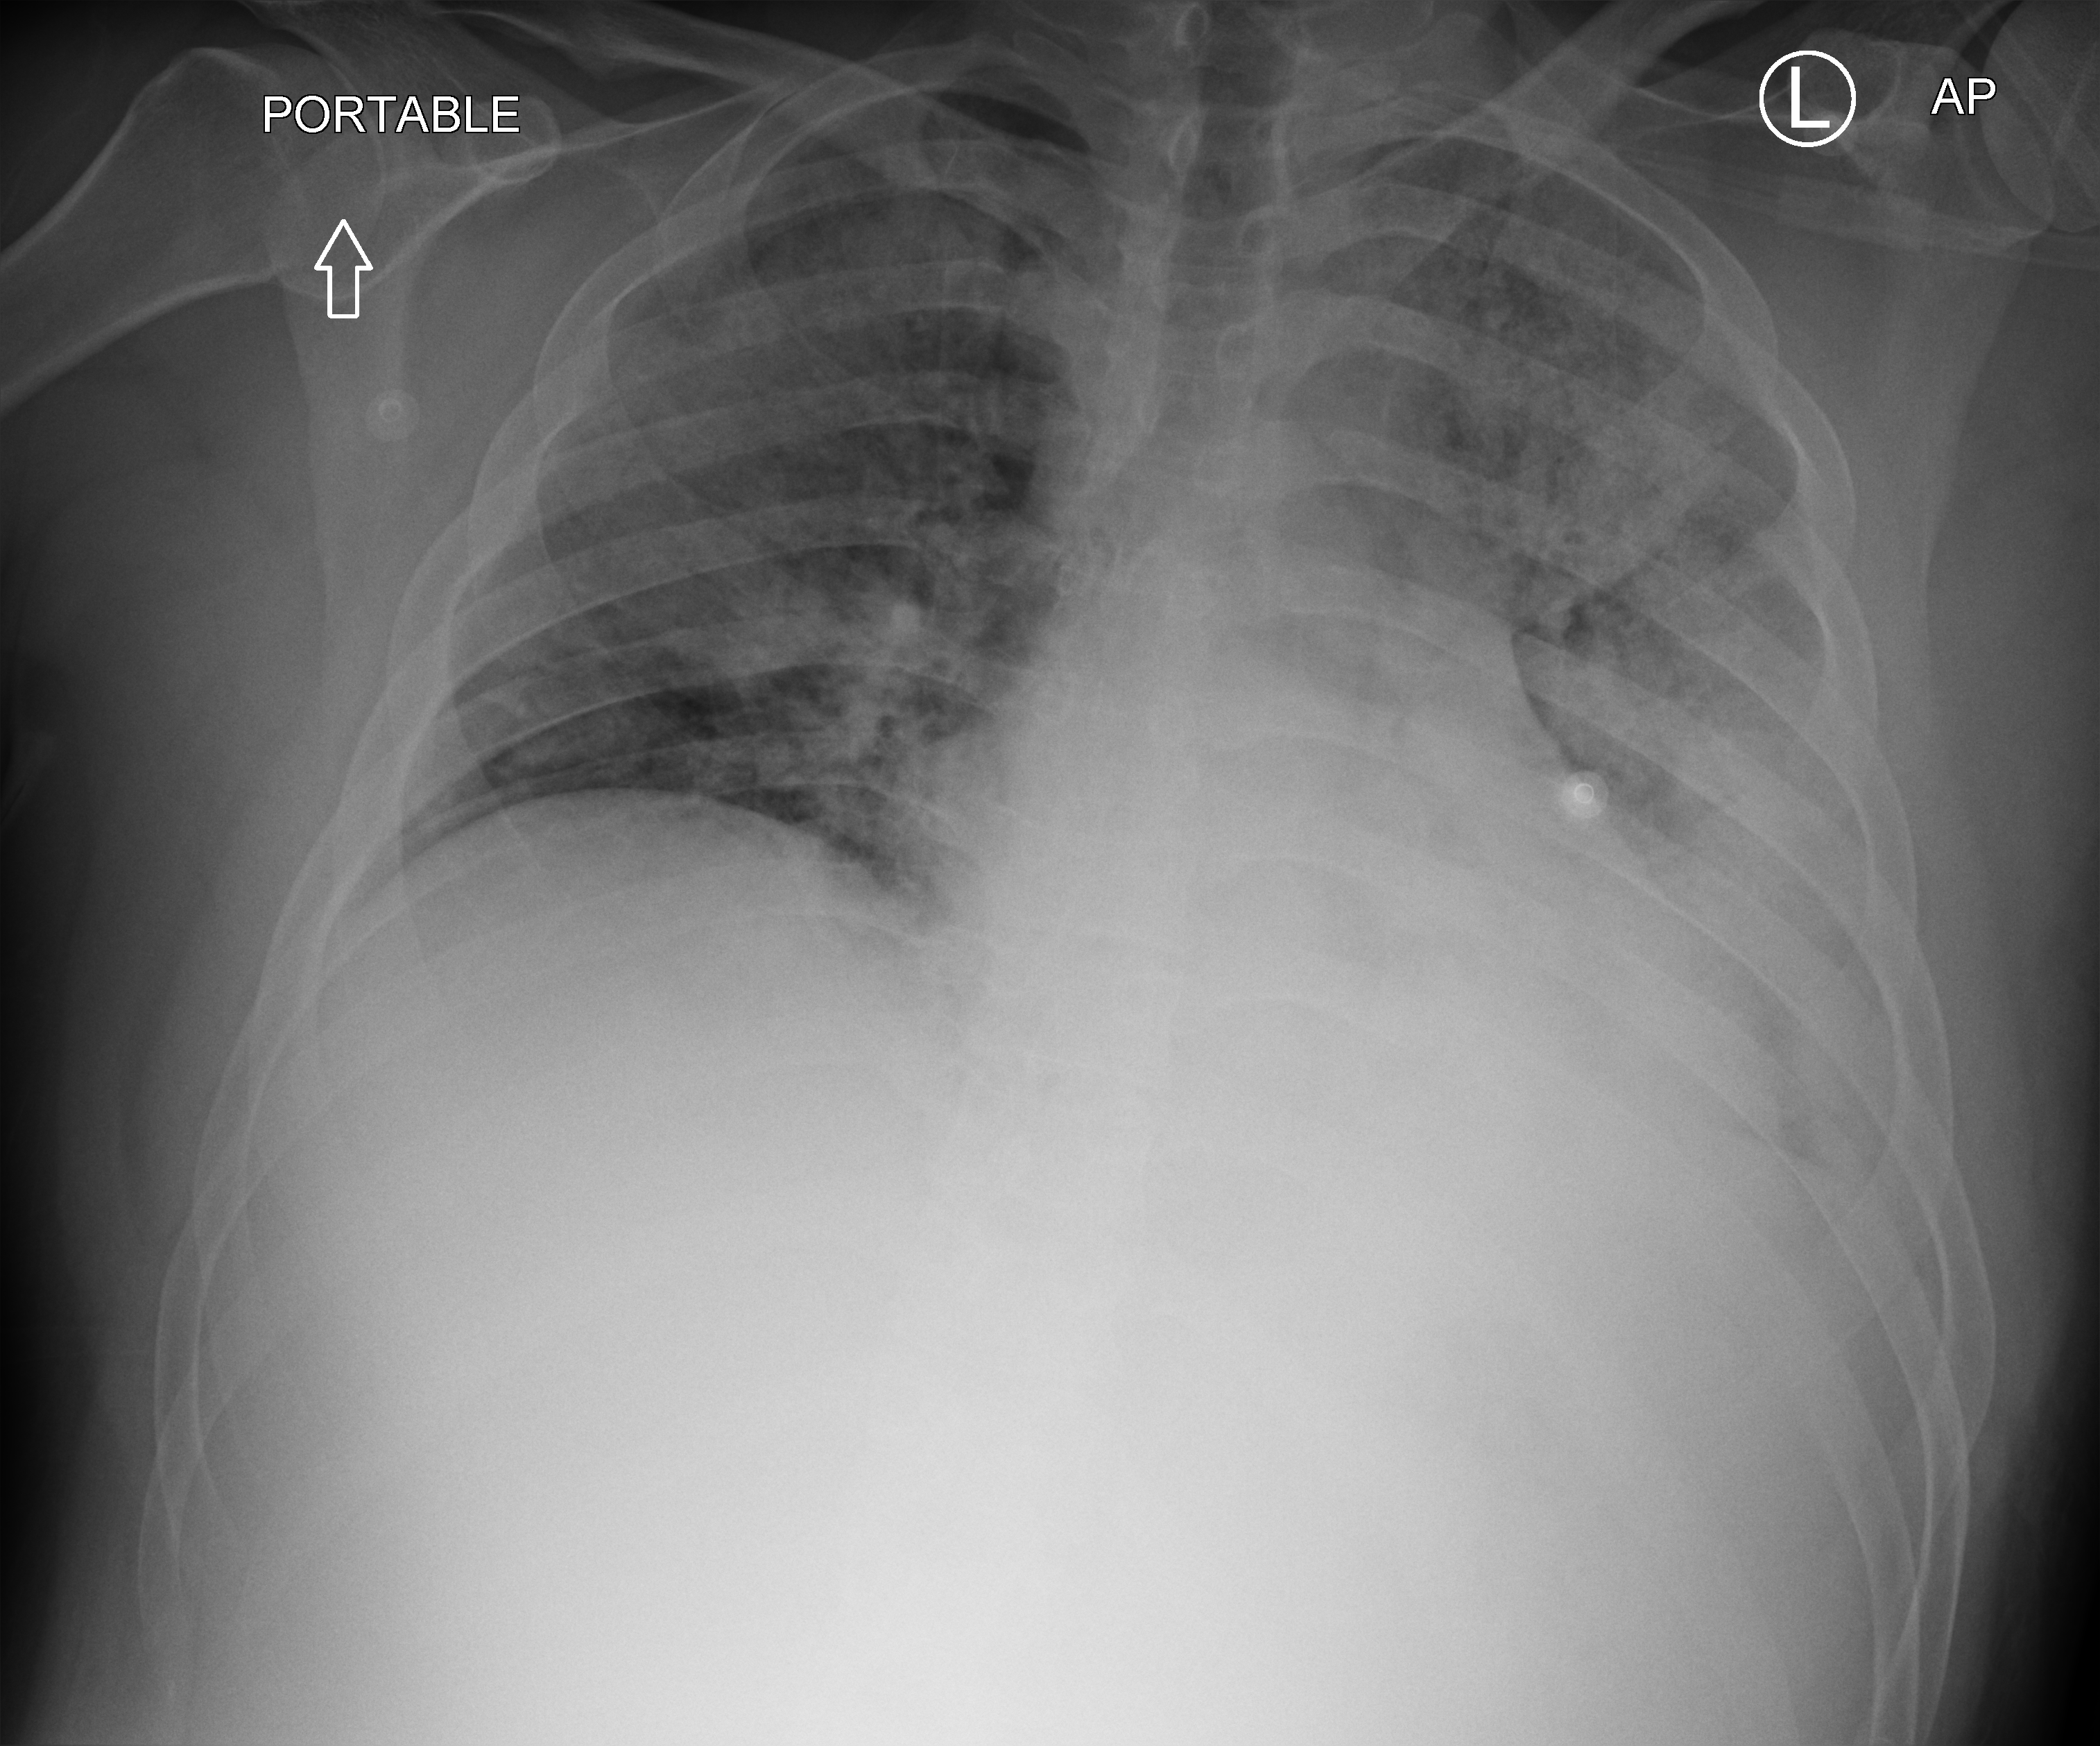
Portable chest radiograph, anteroposterior (AP) projection. Patient hospitalised with COVID-19; male, aged 18–59 years.
From the hospital-stay record, not from the radiograph (when in the stay this image was taken is not recorded): smoking status (admission record): current.